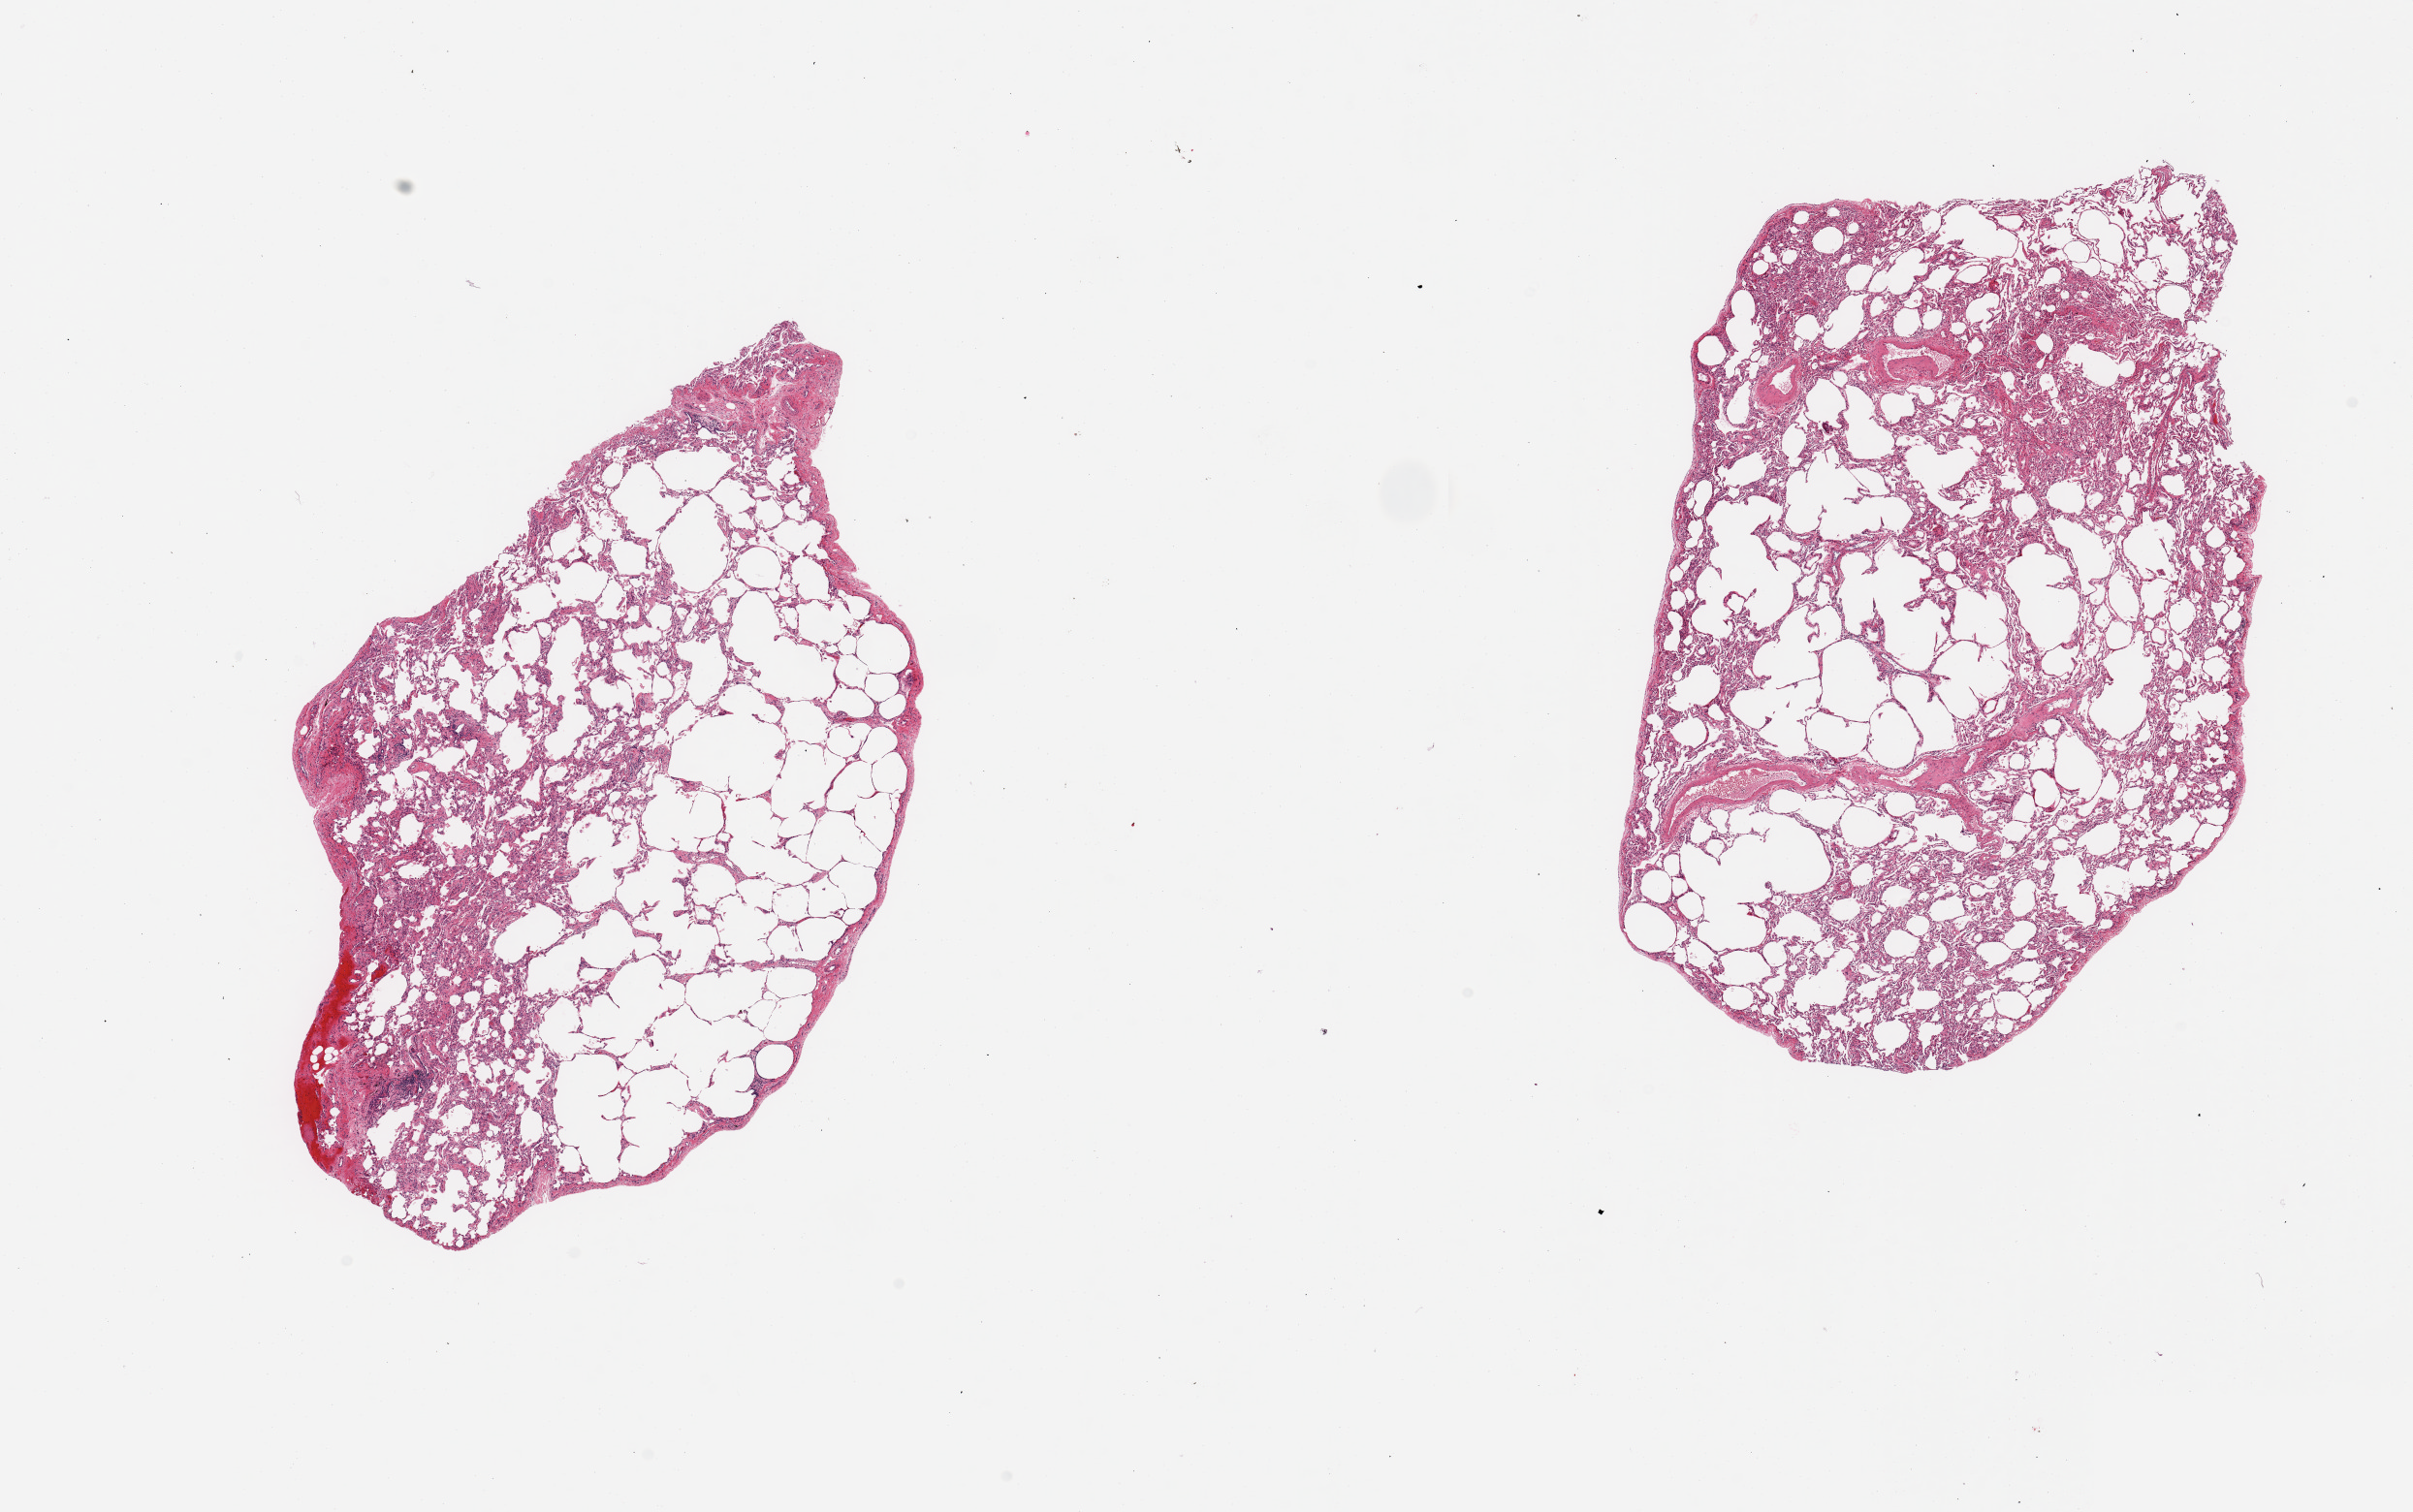
Digitized hematoxylin and eosin (H&E)-stained section — whole scanned area (about 19.7 x 12.3 mm) shown as a low-resolution overview, PAXgene-fixed, paraffin-embedded tissue, sampled site (target tissue): lung, donor tissue sample. Male donor.
• reviewer comment on this tissue sample: 2 pieces; includes pleura (target is 1 cm below pleura), emphysematous change